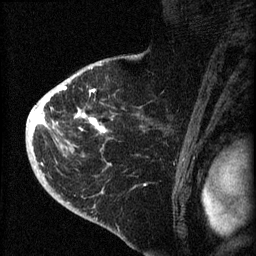
Breast MRI (dynamic contrast-enhanced), one sagittal slice; position 47 of 60 along the scan axis; dynamic contrast-enhanced series, image 2 of 4 at this slice position (ordered by acquisition); 1.5 T; TE 4.2 ms, TR 8.2 ms; 2 mm slice thickness; 256 × 256 image matrix, field of view 180 × 180 mm. Female patient, age 71 years.
Annotated regions visible in this slice (semi-automatically segmented with operator editing):
- analysis volume of interest (the breast-tissue region the enhancement analysis was run in; not a lesion): box from (x=35, y=75) to (x=145, y=190) px
- tumour enhancement mask (voxels above the 70 % enhancement threshold inside the analysis volume of interest): (x=35, y=85)–(x=107, y=164)